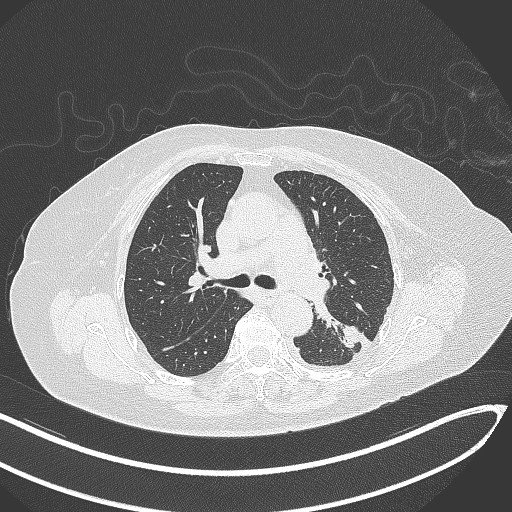
Chest CT, one axial slice. Position 201 of 270 along the scan axis. Lung window (W 1500 / L -600 HU). 512 × 512 image matrix, field of view 400 × 400 mm. Patient: female, 76 years. Case-level facts recorded for this patient, not image findings: clinical TNM (as recorded): T1c N0 M0.
Annotated regions visible in this slice (rectangle marked by the reading radiologist):
- lung tumour (recorded histology: adenocarcinoma): bounding box [x1, y1, x2, y2] px = [338, 322, 359, 352]